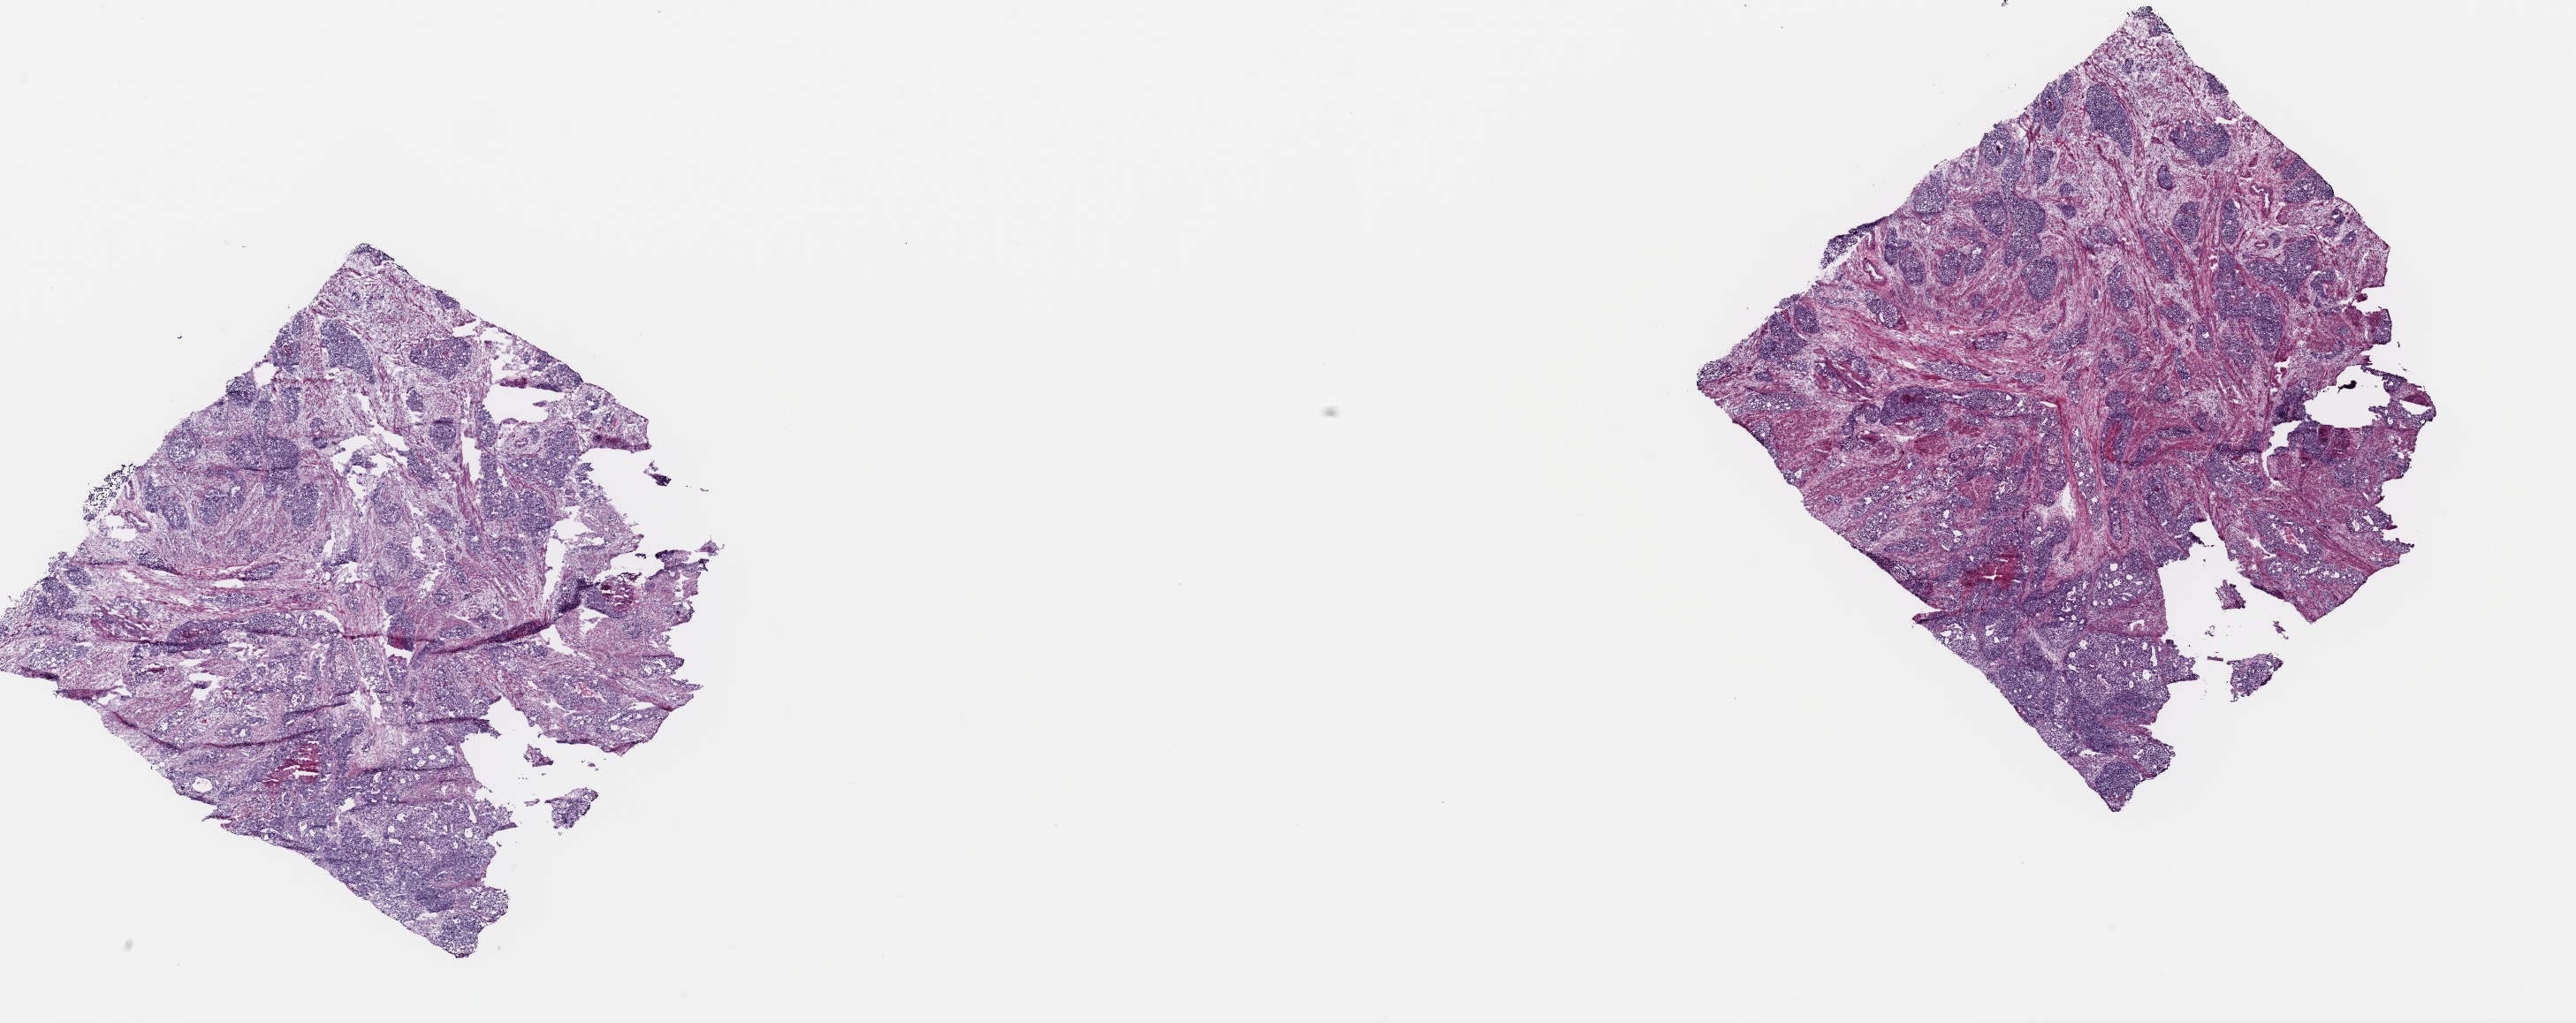
H&E-stained whole-slide image — a low-resolution overview of the entire scanned area, about 23.0 x 9.1 mm (acquisition: 40x scan), frozen section from the top of the tissue portion, sample: primary tumour, uterus. Female, age 53 years at initial diagnosis. Histologic grade: G3 (poorly differentiated). Slide review estimates, as recorded: tumour cells 60%, tumour nuclei 70%, normal cells 30%, stromal cells 0%, necrosis 10%. Inflammatory infiltration, as recorded: lymphocyte infiltration 10%, monocyte infiltration 0%, neutrophil infiltration 10%.
Lymph nodes positive (case pathology): 2 of 30 examined. FIGO stage: IIIC. Pathologic diagnosis: Endometrioid adenocarcinoma, NOS (endometrium).